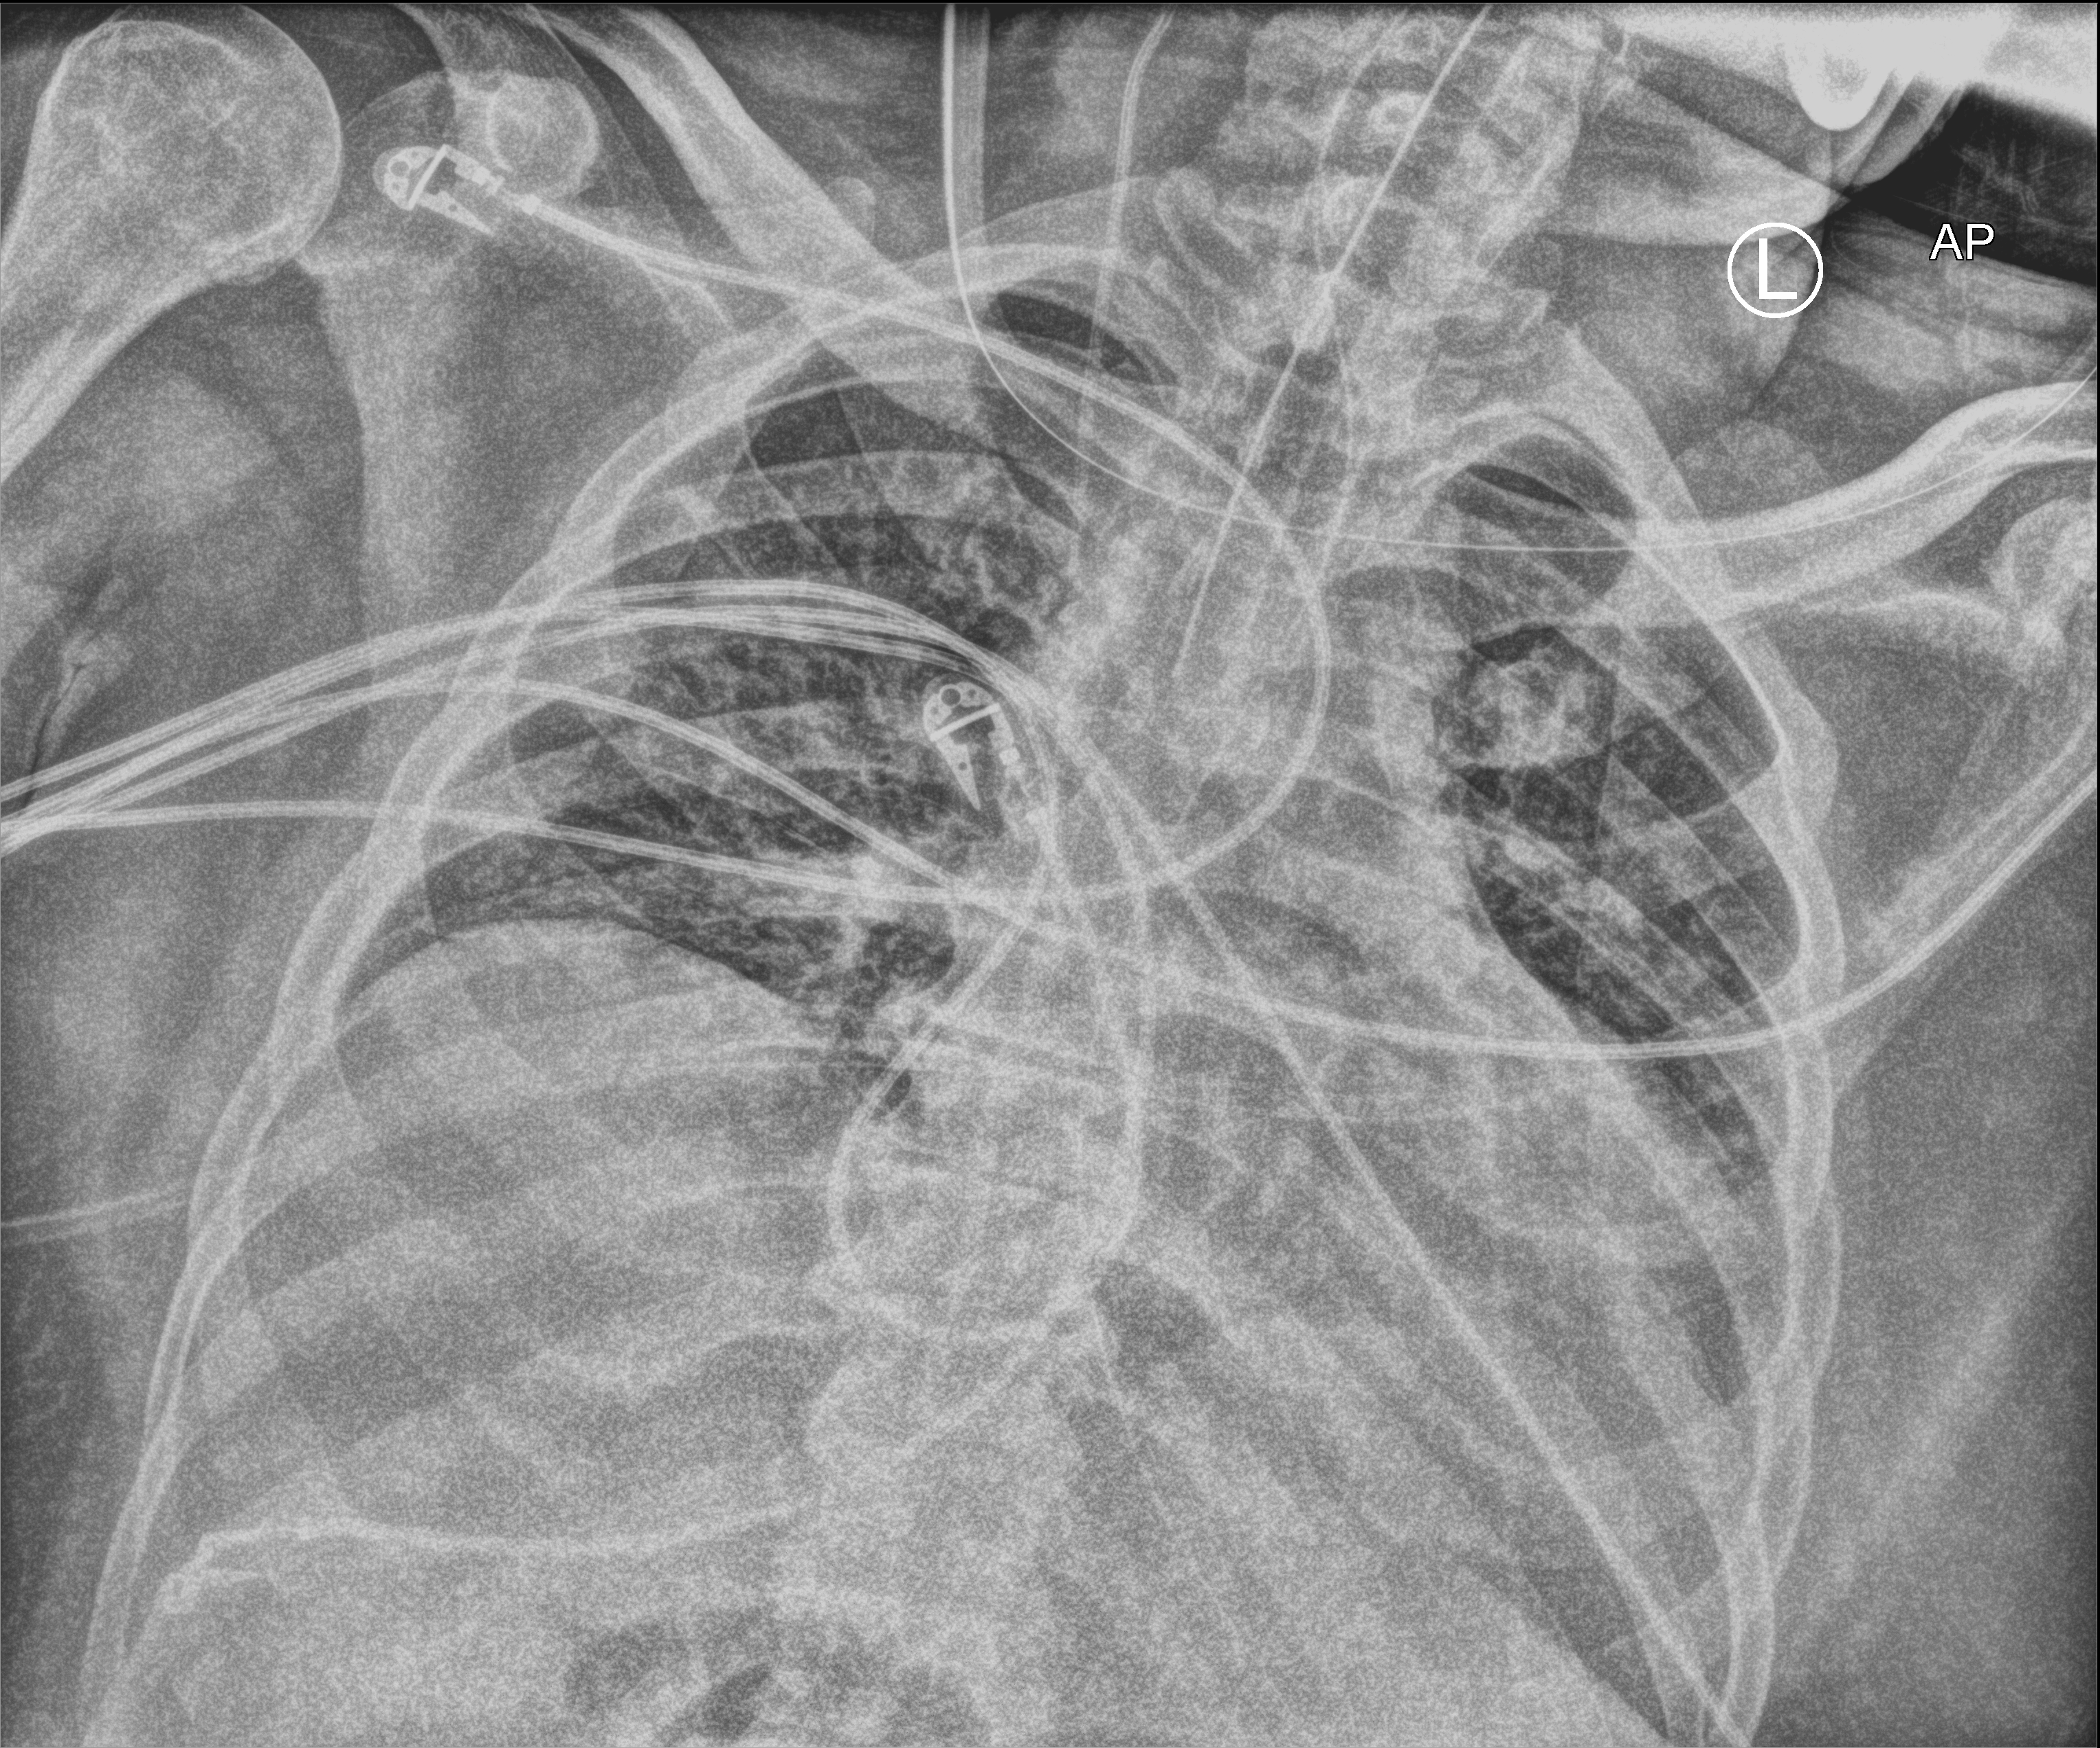
Bedside chest radiograph (computed radiography). Patient hospitalised with COVID-19; male, aged 18–59 years.
Hospital-stay facts (about this admission, not read from this image; timing relative to this image not recorded): admitted to intensive care during this hospital stay: yes; mechanically ventilated during this hospital stay: yes; other chronic lung disease (admission record): no.